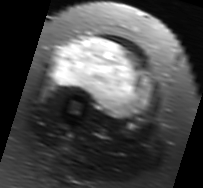
MRI of an extremity soft-tissue mass, one axial slice. Slice 29 of 91 in the series (ordered by position). T2-weighted fat-saturated. MR volume resampled by the dataset authors to the PET/CT grid (not the native acquisition matrix). 203 × 188 image matrix, field of view 198 × 184 mm. Female patient. Case-level facts recorded for this patient, not image findings: histological type: malignant solitary fibrous tumor; grade: intermediate; site of the primary tumour: right thigh.
Structures marked on this image (expert contour drawn on MRI and transferred to this co-registered scan by the dataset authors):
- gross tumour volume including surrounding oedema: bounding box (x1, y1, x2, y2) in pixels: (51, 37, 155, 123)
- gross tumour volume (mass): (54, 37, 152, 116)